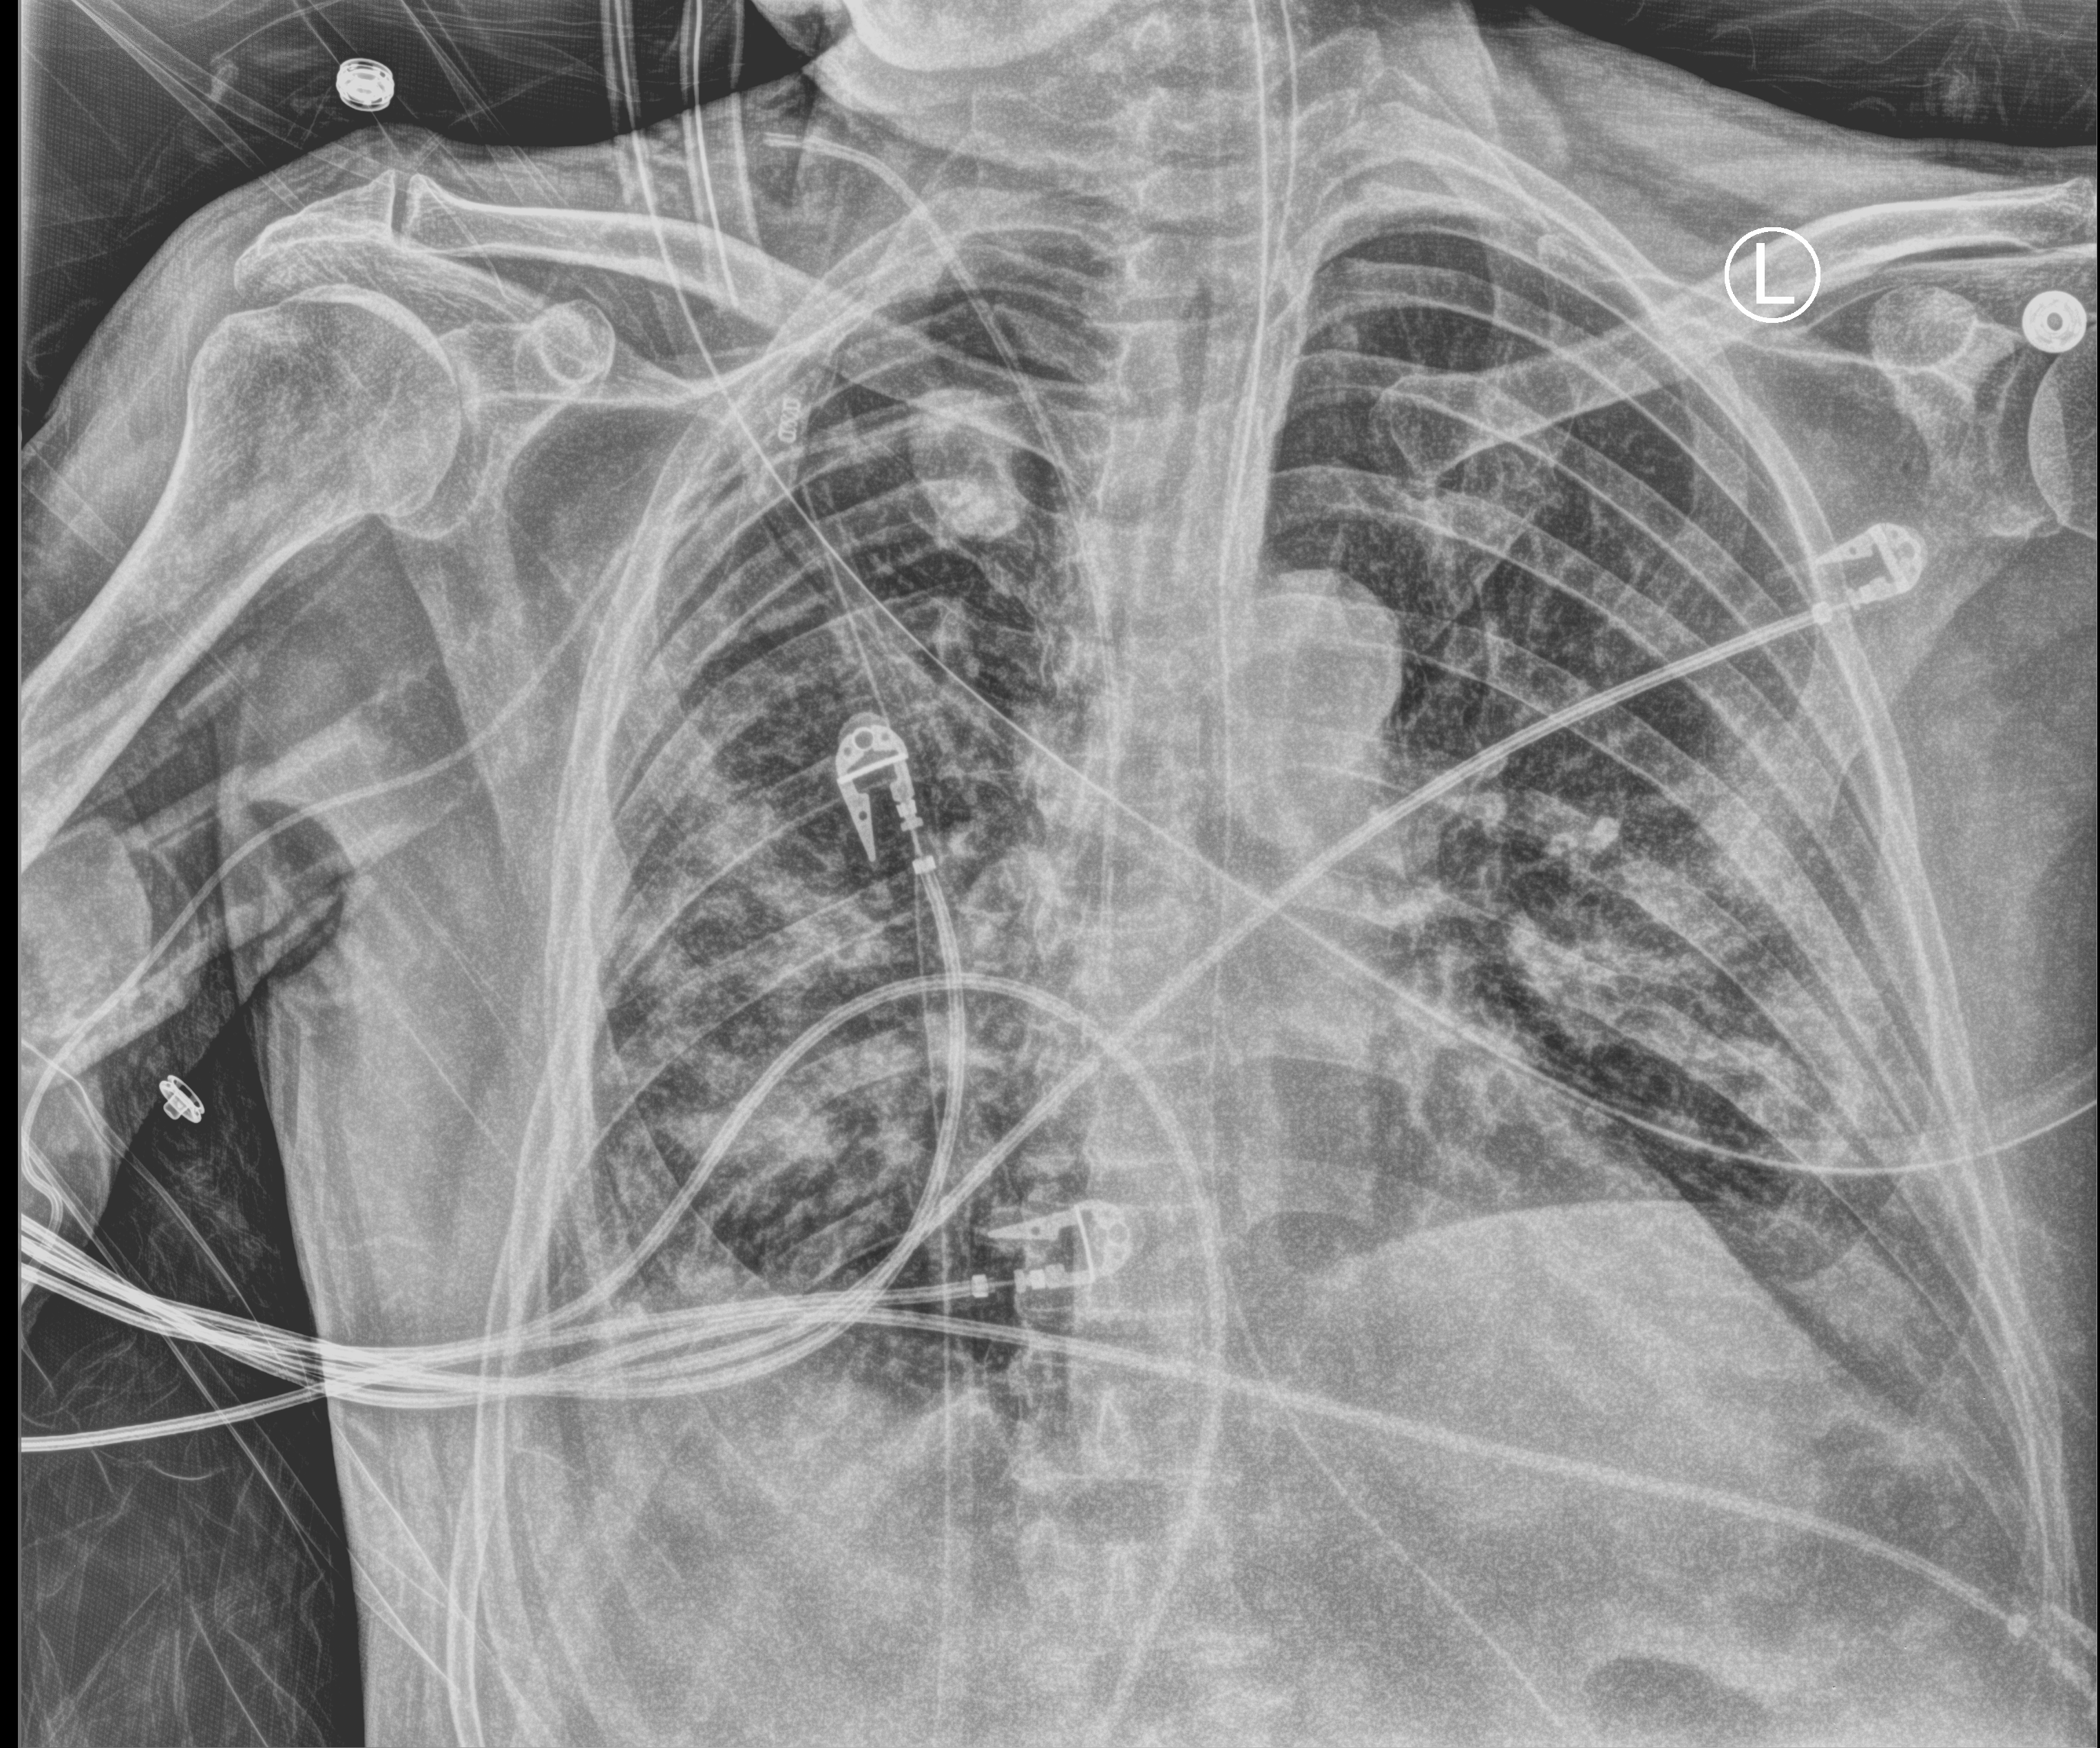
Bedside chest radiograph (computed radiography); anteroposterior (AP) projection. Male patient hospitalised with COVID-19, age 75–90 years.
Hospital-stay facts (about this admission, not read from this image; timing relative to this image not recorded):
- admitted to intensive care during this hospital stay: yes